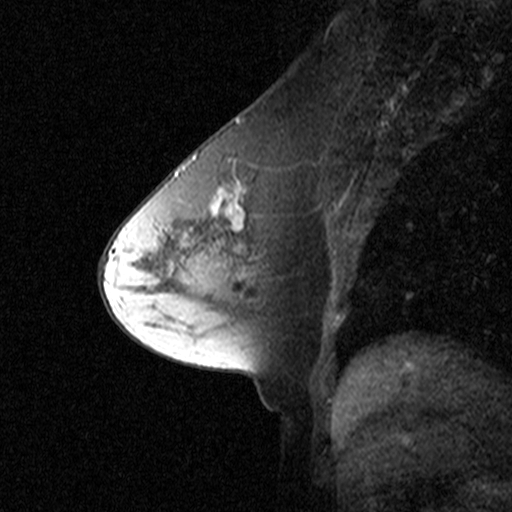
Breast MRI (dynamic contrast-enhanced), one sagittal slice; position 23 of 44 along the scan axis; dynamic contrast-enhanced study with each time point stored as its own series, time point 2 of 3 at this slice position (early post-contrast, ordered by acquisition time); 1.5 T; TE 4.5 ms, TR 11 ms; 3 mm slice thickness; 512 × 512 image matrix, field of view 200 × 200 mm. Patient: female, 53 years. Case-level facts recorded for this patient, not image findings: setting: breast cancer imaged before/during neoadjuvant chemotherapy; receptor status: HR-positive, HER2-negative.
Annotated regions visible in this slice (semi-automatic segmentation, software-assisted and operator-edited):
- analysis volume of interest (the breast-tissue region the enhancement analysis was run in; not a lesion): bounding box <170,150,277,273> (left, top, right, bottom; pixels)
- tumour enhancement mask (voxels above the 90 % enhancement threshold inside the analysis volume of interest): <176,154,248,251>